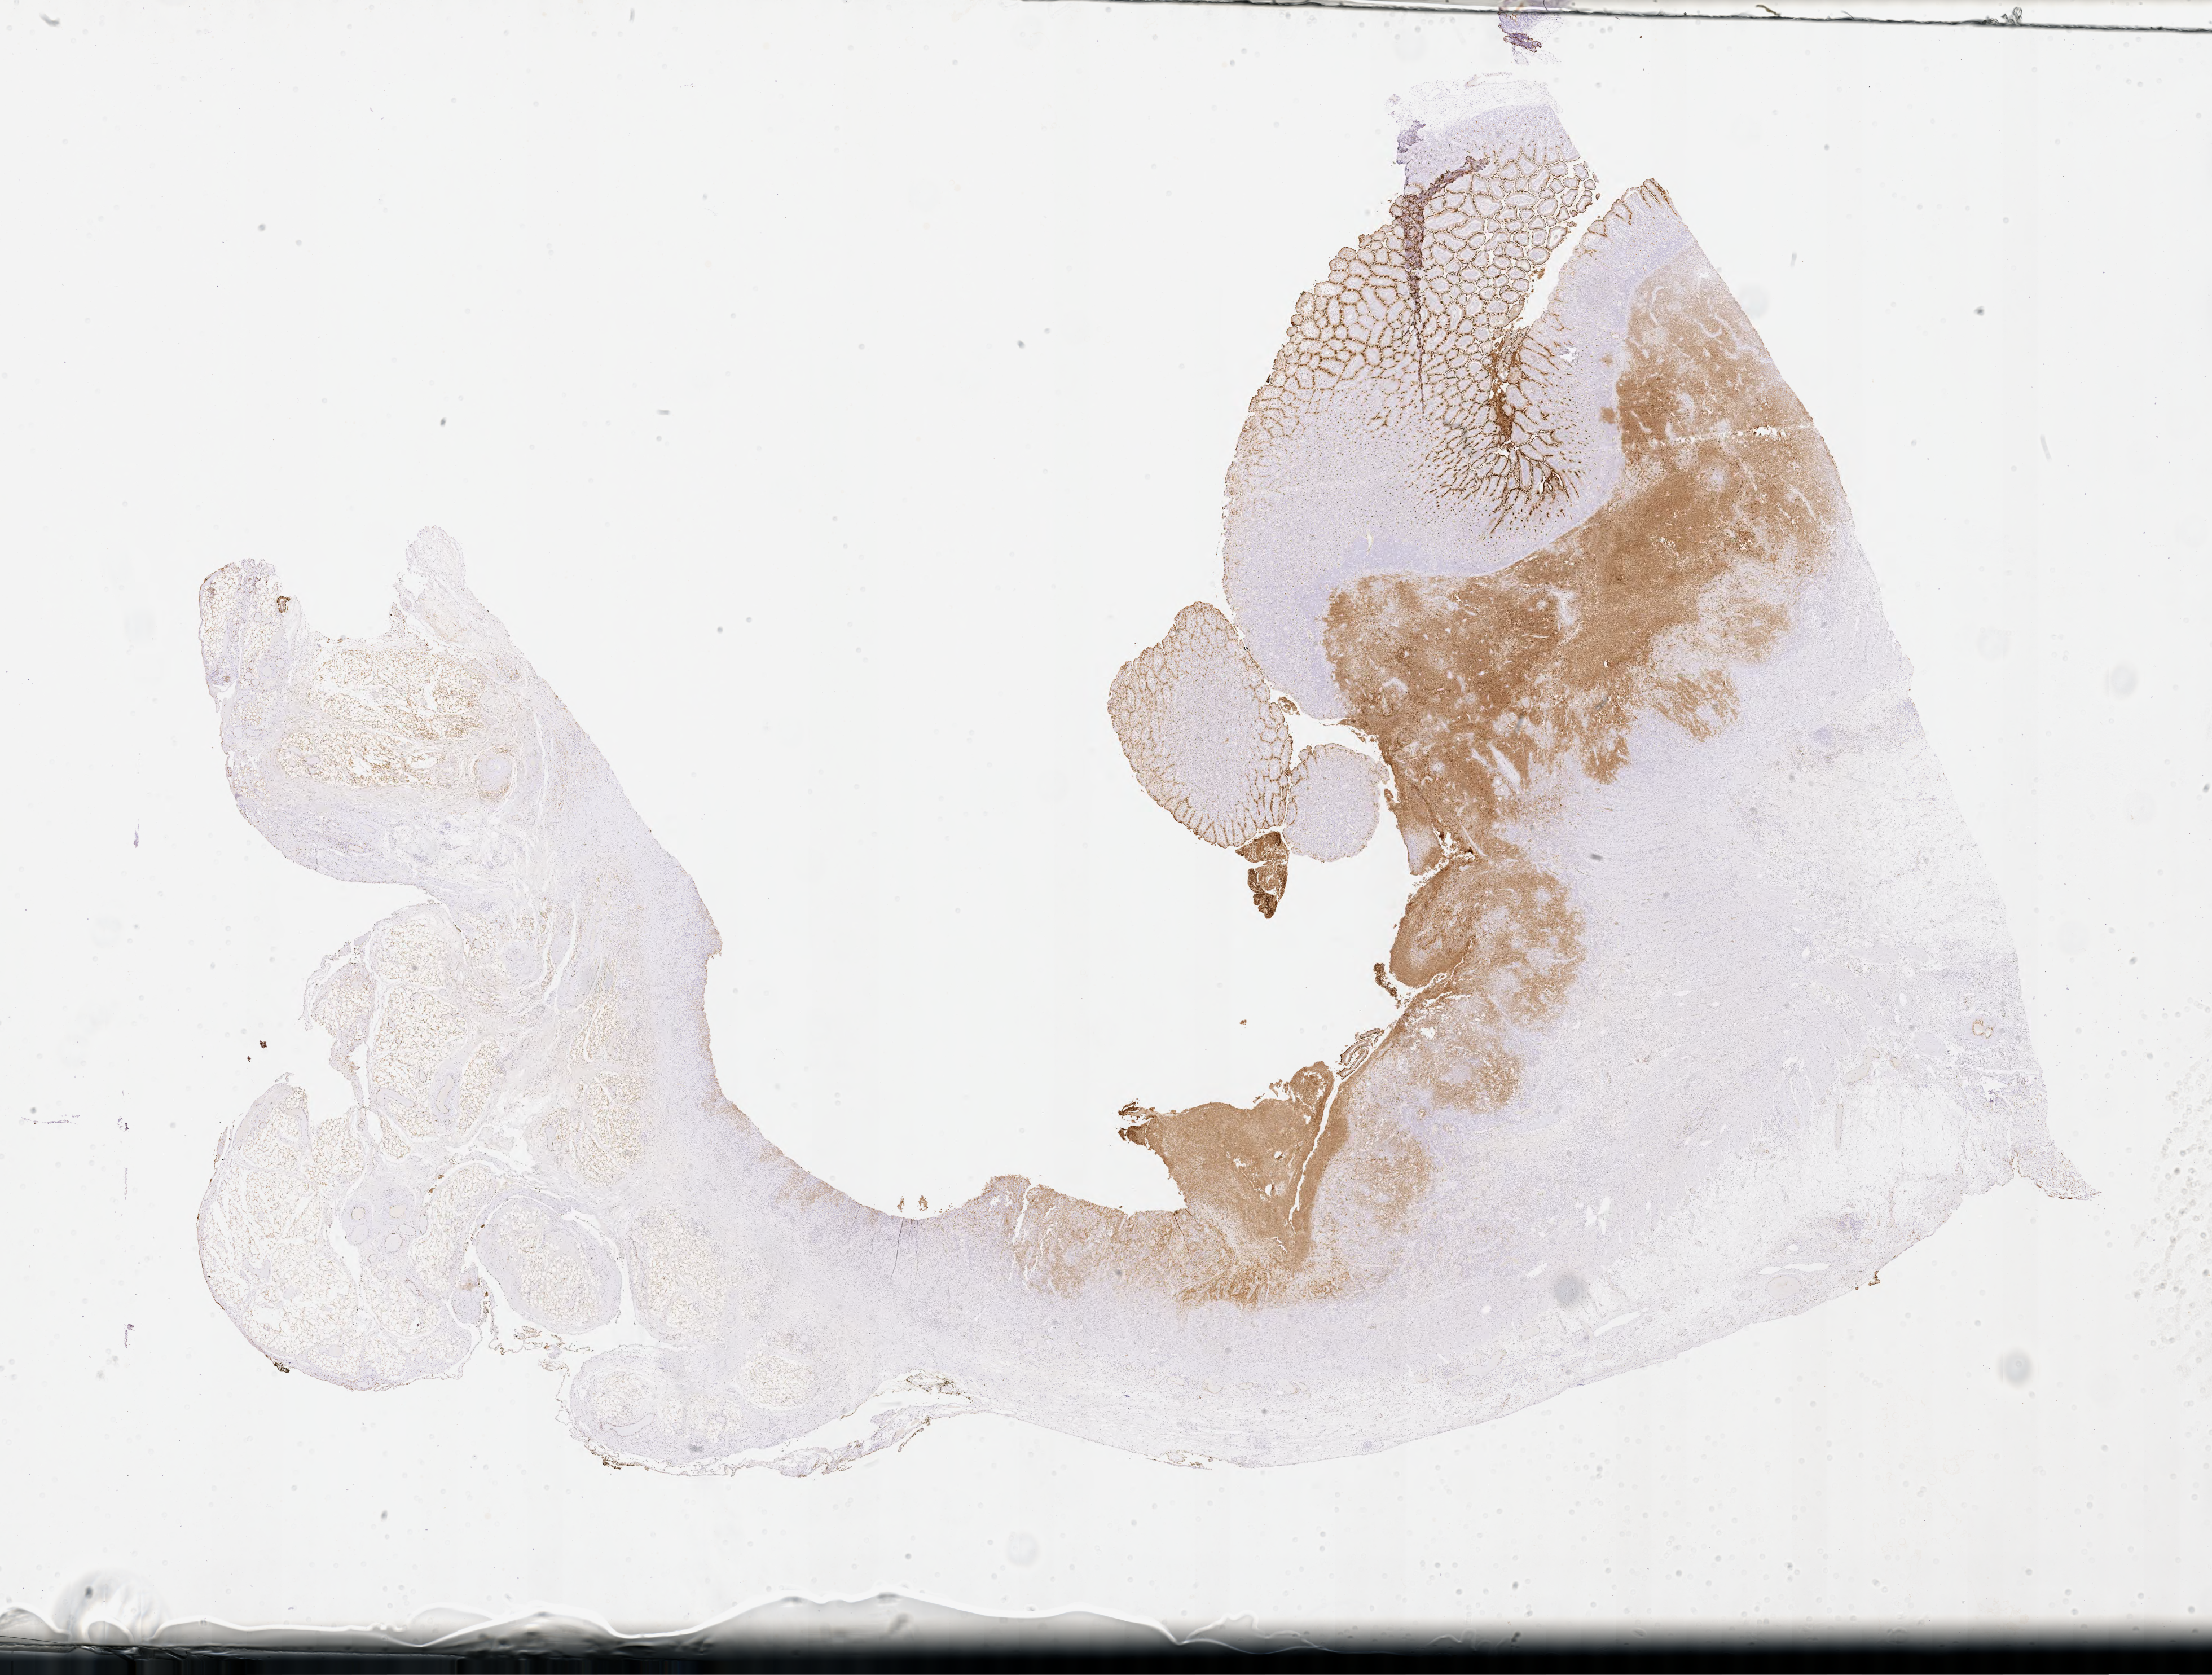
Whole-slide image, immunohistochemical stain for CD10, a low-resolution overview of the entire scanned area, about 31.7 x 24.0 mm, tumor tissue. Patient: female, age 44 years.
Histologic diagnosis: Burkitt lymphoma, NOS.